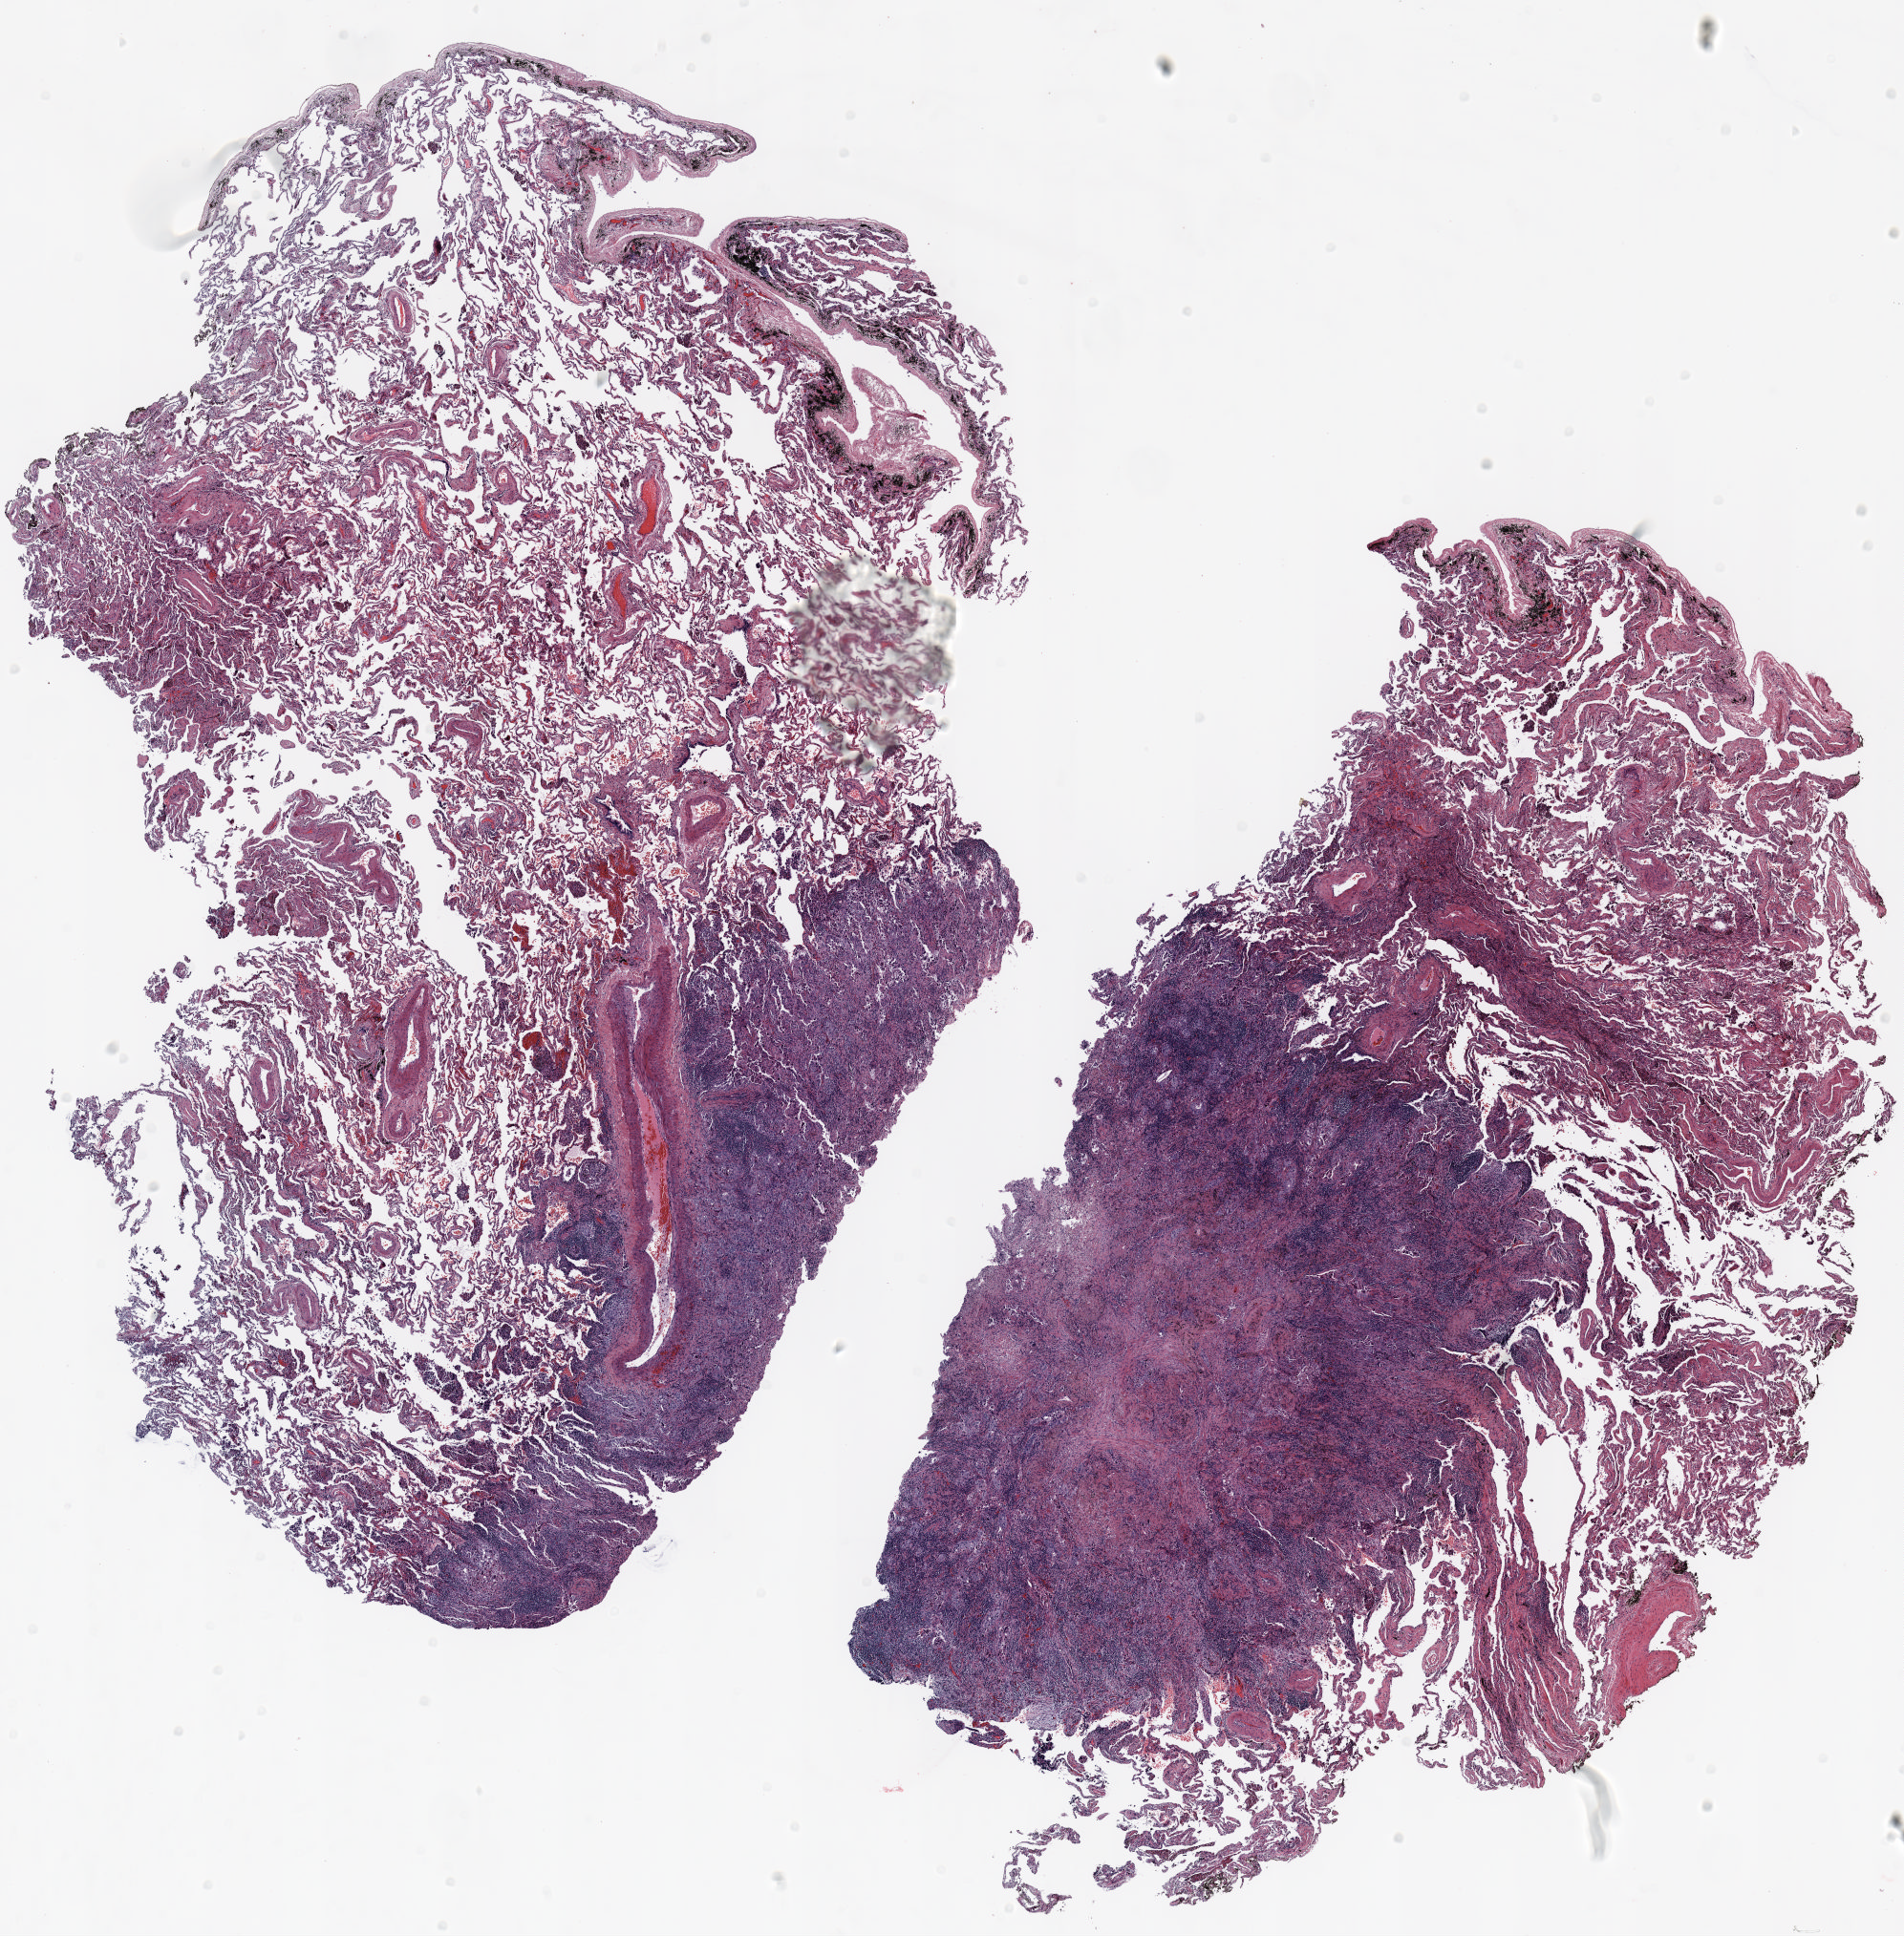
Whole-slide histology image, Hematoxylin and eosin (H&E) stained, a low-resolution overview of the entire scanned area, about 16.0 x 16.3 mm, FFPE section, lung tissue. Female patient, aged 72 at enrolment. Current smoker at enrolment. Grade: poorly differentiated (G3).
Primary tumour location (clinical record): right upper lobe. Tumour size (pathology): 9 mm. Stage (AJCC 6th edition): IA. Participant's lung-cancer diagnosis: Non-small cell carcinoma.